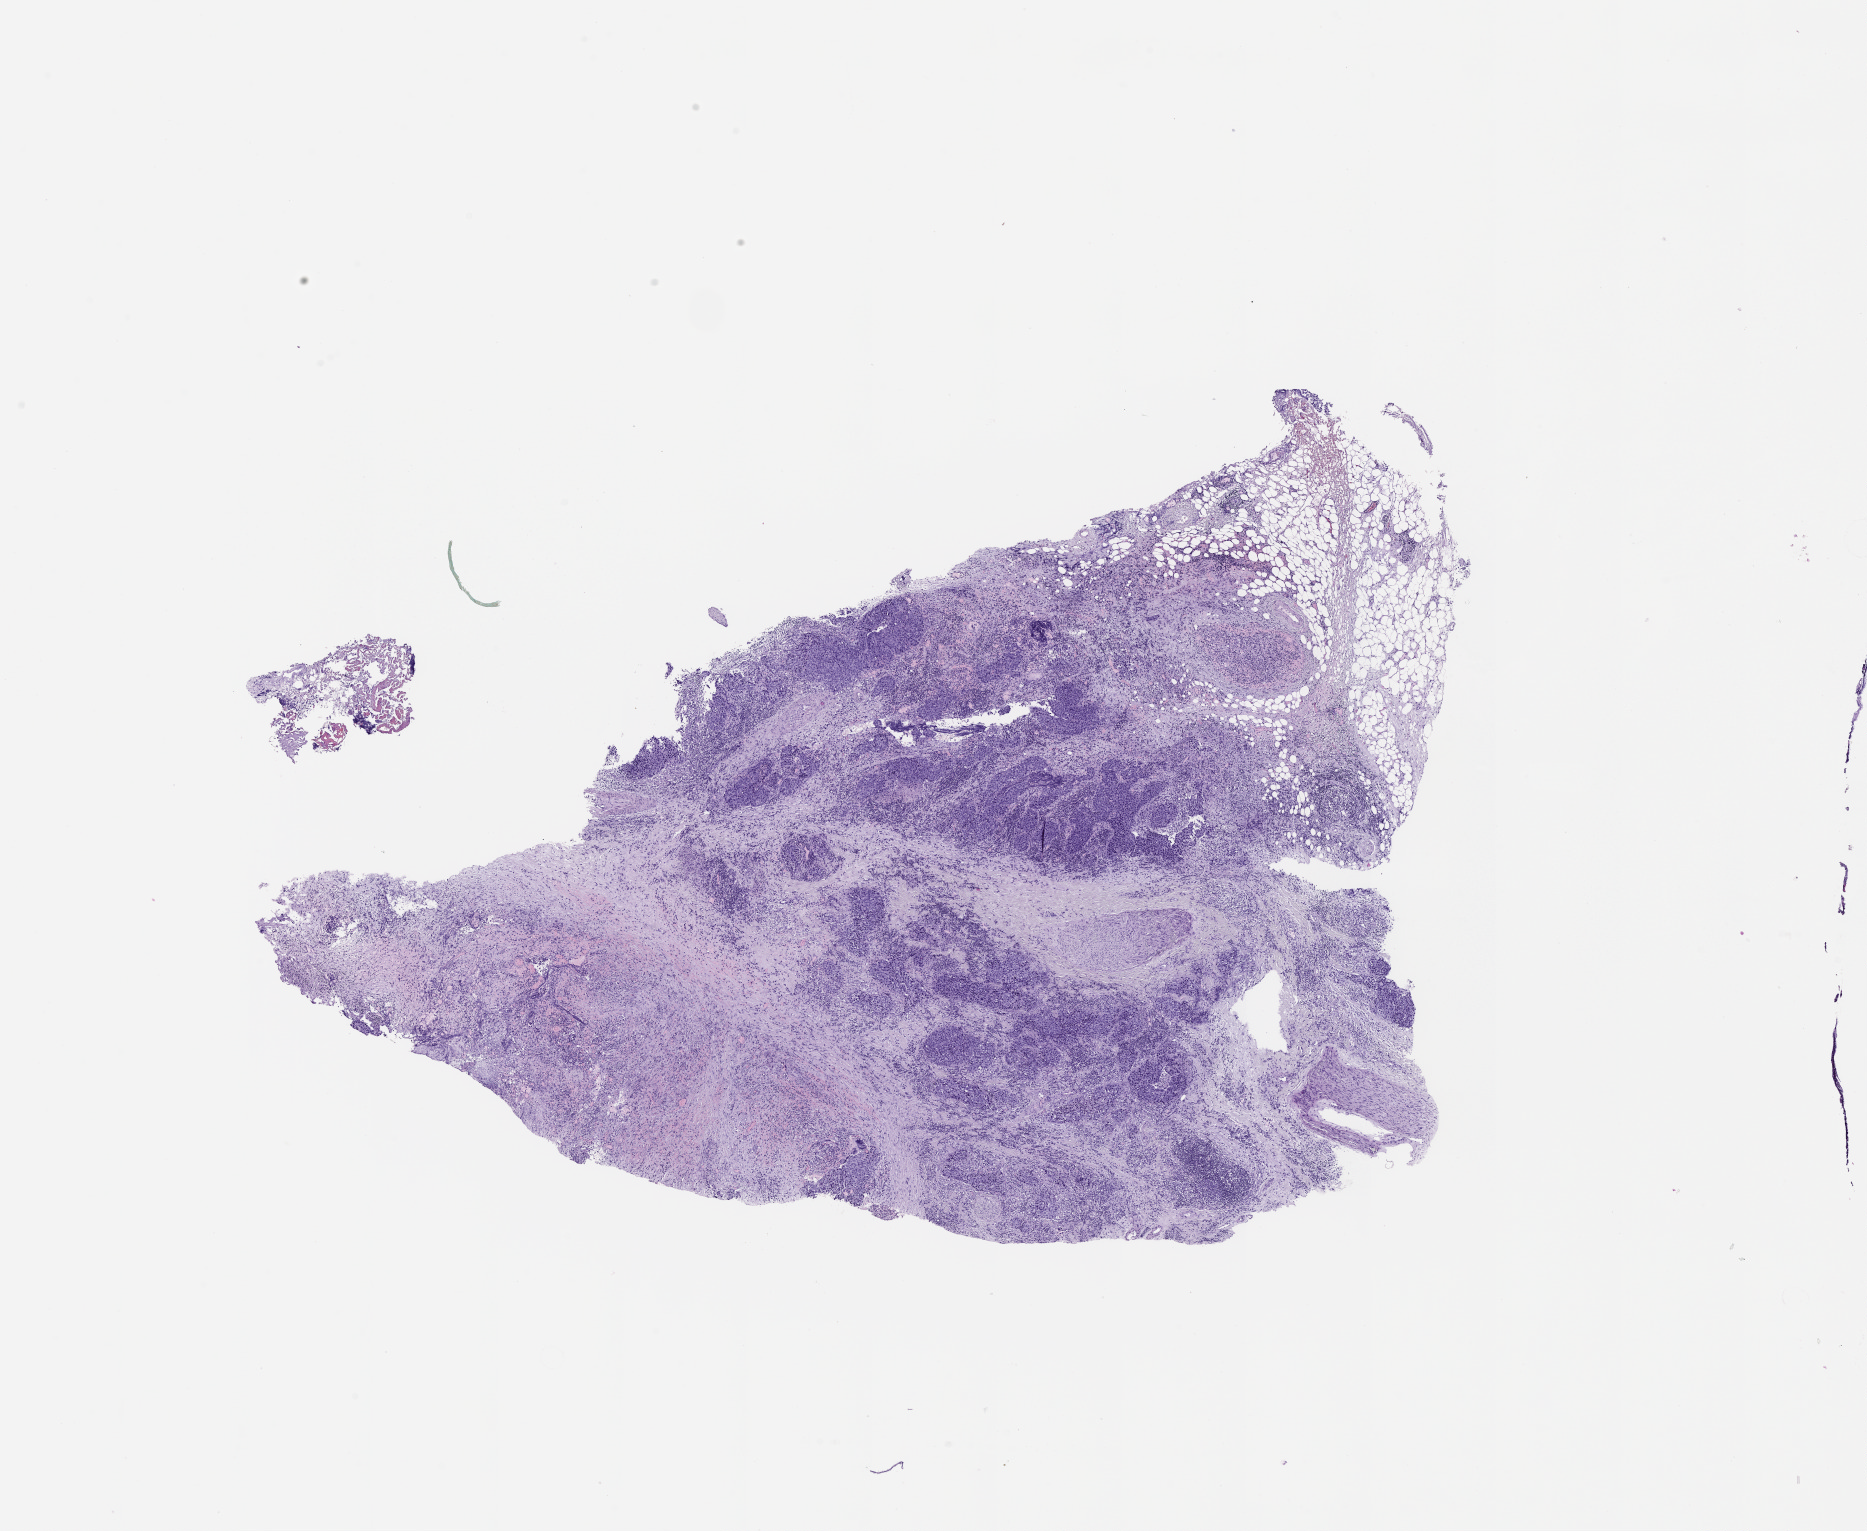
H&E-stained whole-slide image, shown as a low-resolution overview of the whole scanned area (about 15.0 x 12.3 mm); tumour tissue sample, lung. Male, 63 y/o.
- patient diagnosis (cohort enrolment): squamous cell carcinoma (lung)